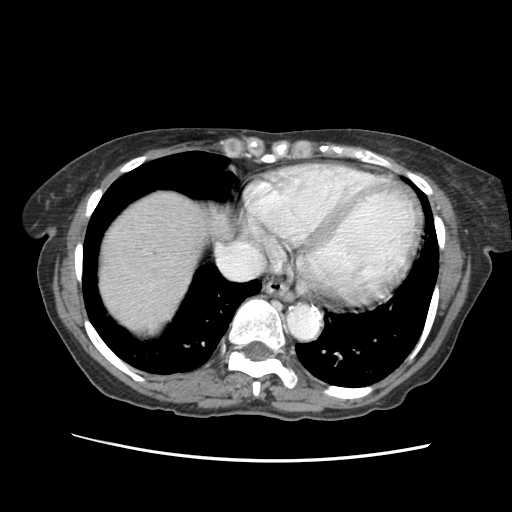
Contrast-enhanced abdominal CT (liver protocol), one axial slice; position 55 of 63 along the scan axis; reconstruction kernel STANDARD; 120 kVp; soft-tissue window (W 400 / L 40 HU); 512 × 512 image matrix, field of view 340 × 340 mm. From the clinical record (not read from this slice): diagnosis: hepatocellular carcinoma (patient treated with transarterial chemoembolisation; whether this scan precedes or follows treatment is not stated here); TNM stage (as recorded): Stage-I; Child-Pugh class: B.
Structures marked on this image (semi-automatically segmented with operator editing):
- liver parenchyma outside the tumour (the mass and vessels are separate outlines, so this box may not span the whole liver): bounding box [x1, y1, x2, y2] px = [100, 190, 208, 324]